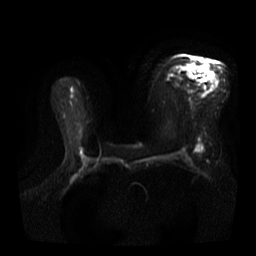
Breast MRI, one axial slice. Position 22 of 40 along the scan axis. Diffusion-weighted series; image 2 of 4 stored at this slice position (different b-values; order by instance number). 3 T. 256 × 256 image matrix. Female patient.
Structures marked on this image (expert manual segmentation):
- tumour on diffusion-weighted imaging: box from (x=198, y=64) to (x=210, y=74) px